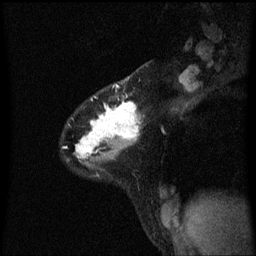
Breast MRI (dynamic contrast-enhanced), one sagittal slice. Slice 44 of 60 in the series (ordered by position). Dynamic contrast-enhanced series, image 2 of 3 at this slice position (ordered by acquisition). 1.5 T. TE 4.2 ms, TR 8.4 ms. 256 × 256 image matrix, field of view 200 × 200 mm. Patient: female, 32 years.
Outlined on this slice (semi-automatically segmented with operator editing):
- analysis volume of interest (the breast-tissue region the enhancement analysis was run in; not a lesion): bounding box <67,76,141,167> (left, top, right, bottom; pixels)
- tumour enhancement mask (voxels above the 70 % enhancement threshold inside the analysis volume of interest): <76,102,141,159>